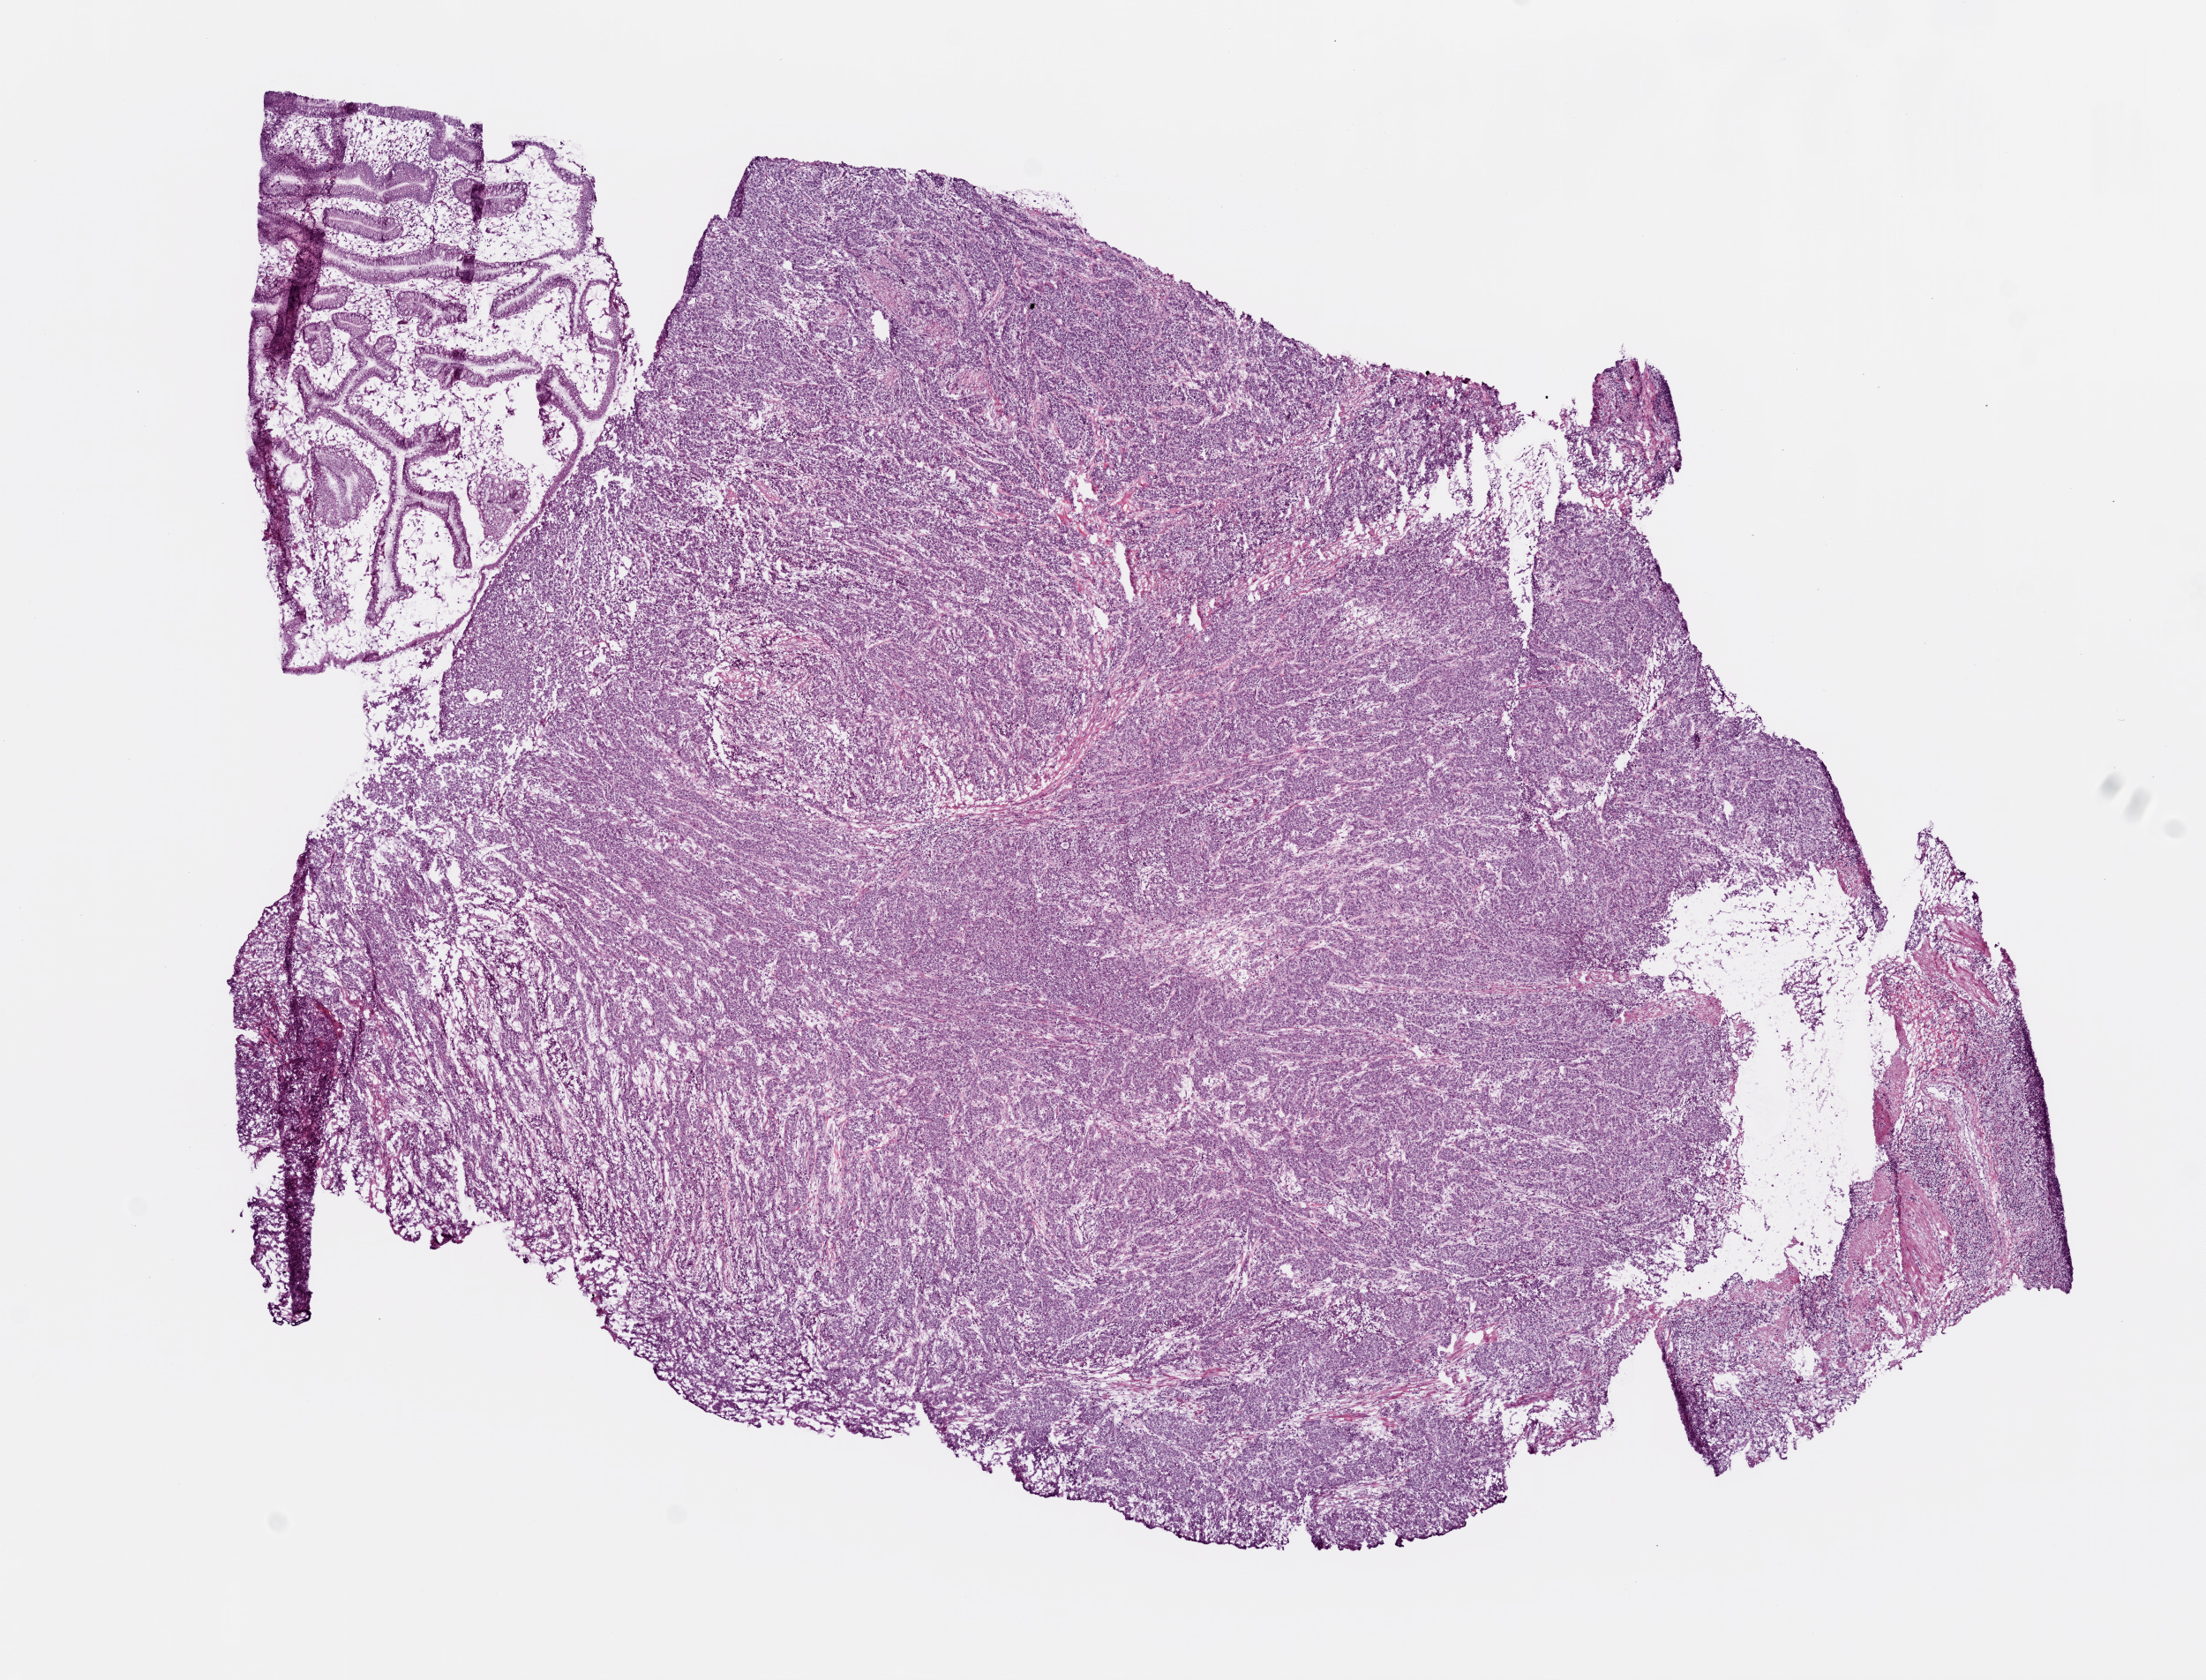
H&E-stained whole-slide image — whole scanned area (about 10.0 x 7.6 mm, slide scanned at 20x) shown as a low-resolution overview, frozen section, primary tumour sample from the stomach. Male, age 58 years at initial diagnosis. Histologic grade: G3 (poorly differentiated). Composition of this section per pathologist review: tumour cells 77%, tumour nuclei 80%, normal cells 10%, stromal cells 10%, necrosis 3%.
AJCC pathologic stage: IV (5th edition). Diagnosis: Adenocarcinoma, intestinal type (gastric antrum). Lymph nodes positive (case pathology): 1 of 24 examined.